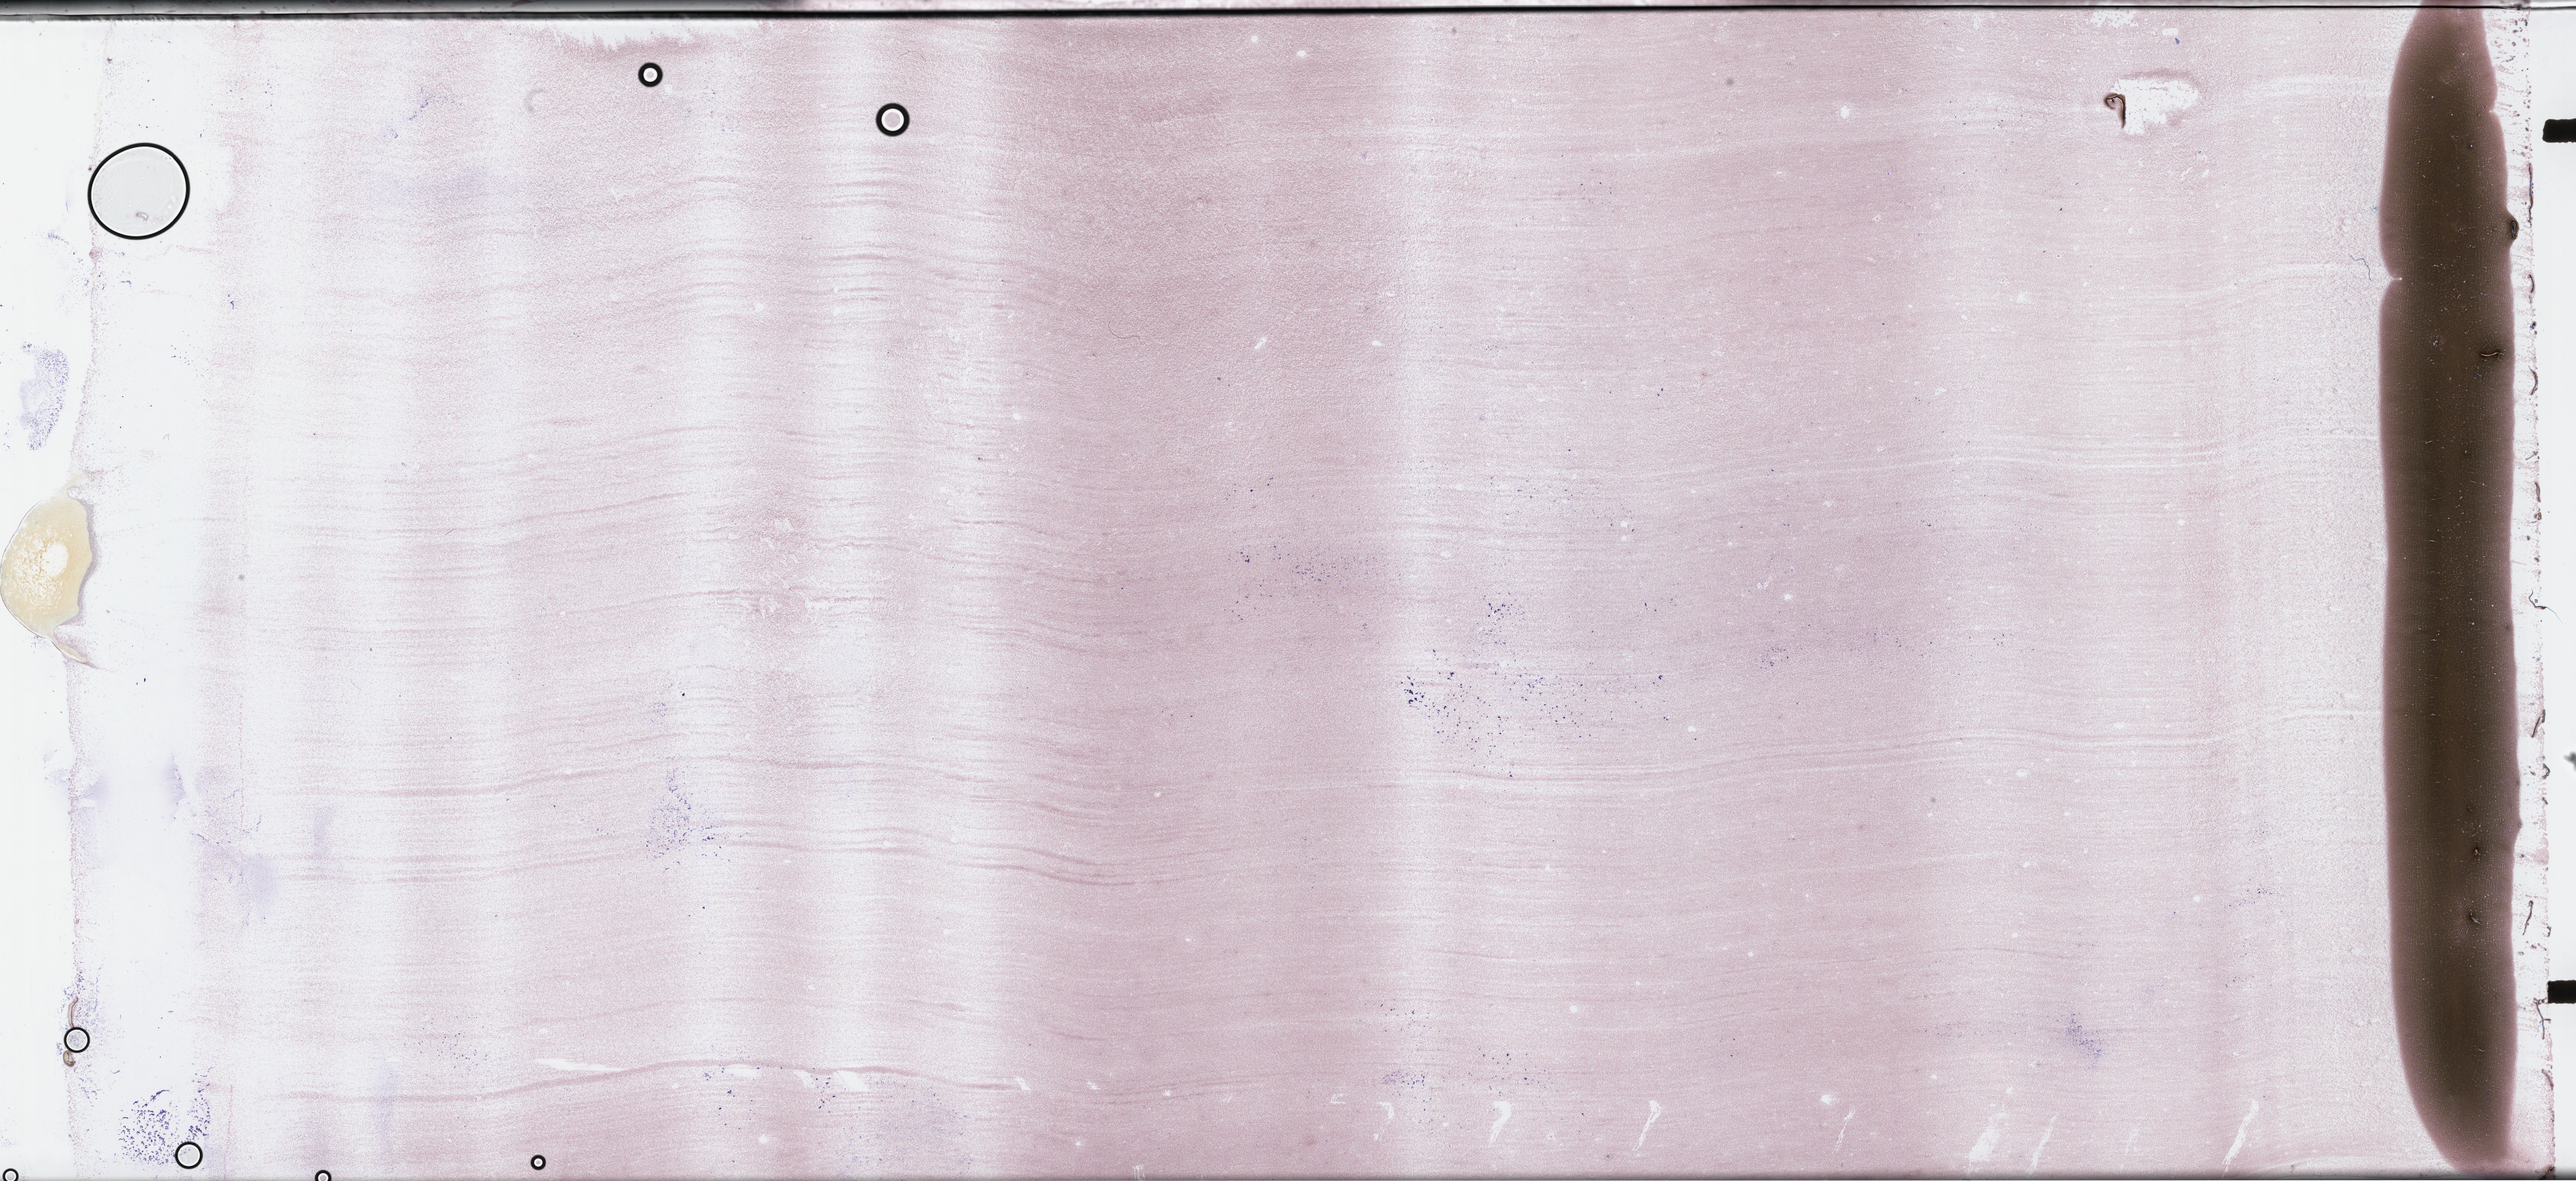
Whole-slide image of a bone marrow smear, Wright–Giemsa stain — a low-resolution overview of the entire scanned area, about 52.3 x 24.0 mm. Smear from an EDTA sample. Specimen time point: collected at baseline (before treatment). Male patient.
From a patient with: Plasma Cell Myeloma.